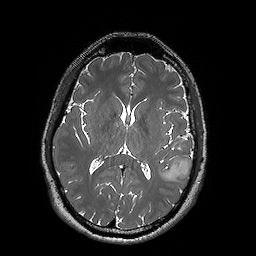
Brain MRI from a brain-tumour surgery series, one axial slice; slice 84 of 192 in the series (ordered by position); 256 × 256 image matrix. Case-level facts recorded for this patient, not image findings: histopathology: Oligodendroglioma; WHO grade: 2; IDH mutation: yes; tumour location: Left Posterior Temporal.
Outlined on this slice (manually delineated by an expert):
- tumour: bounding box <159,159,193,180> (left, top, right, bottom; pixels)